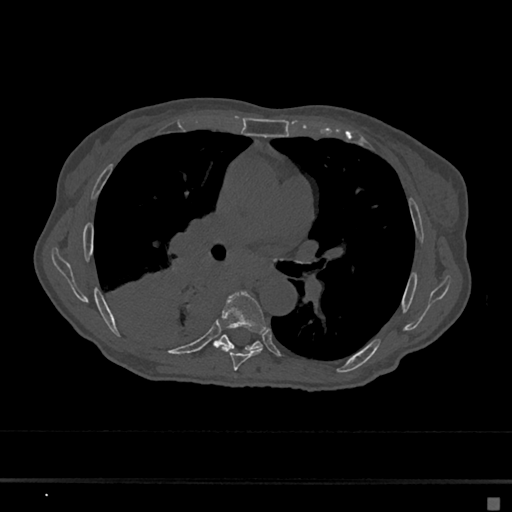
CT including the spine, one axial slice. Slice 400 of 797 in the series (ordered by position). Bone window (W 1800 / L 400 HU). 0.5 mm slice thickness. 512 × 512 image matrix. Patient: female, 68 years. From the clinical record (not read from this slice): primary cancer: renal.
Annotated regions visible in this slice (semi-automatic segmentation, software-assisted and operator-edited):
- T6 vertebra: bounding box (x1, y1, x2, y2) in pixels: (221, 291, 267, 371)
- T7 vertebra: (213, 335, 263, 351)